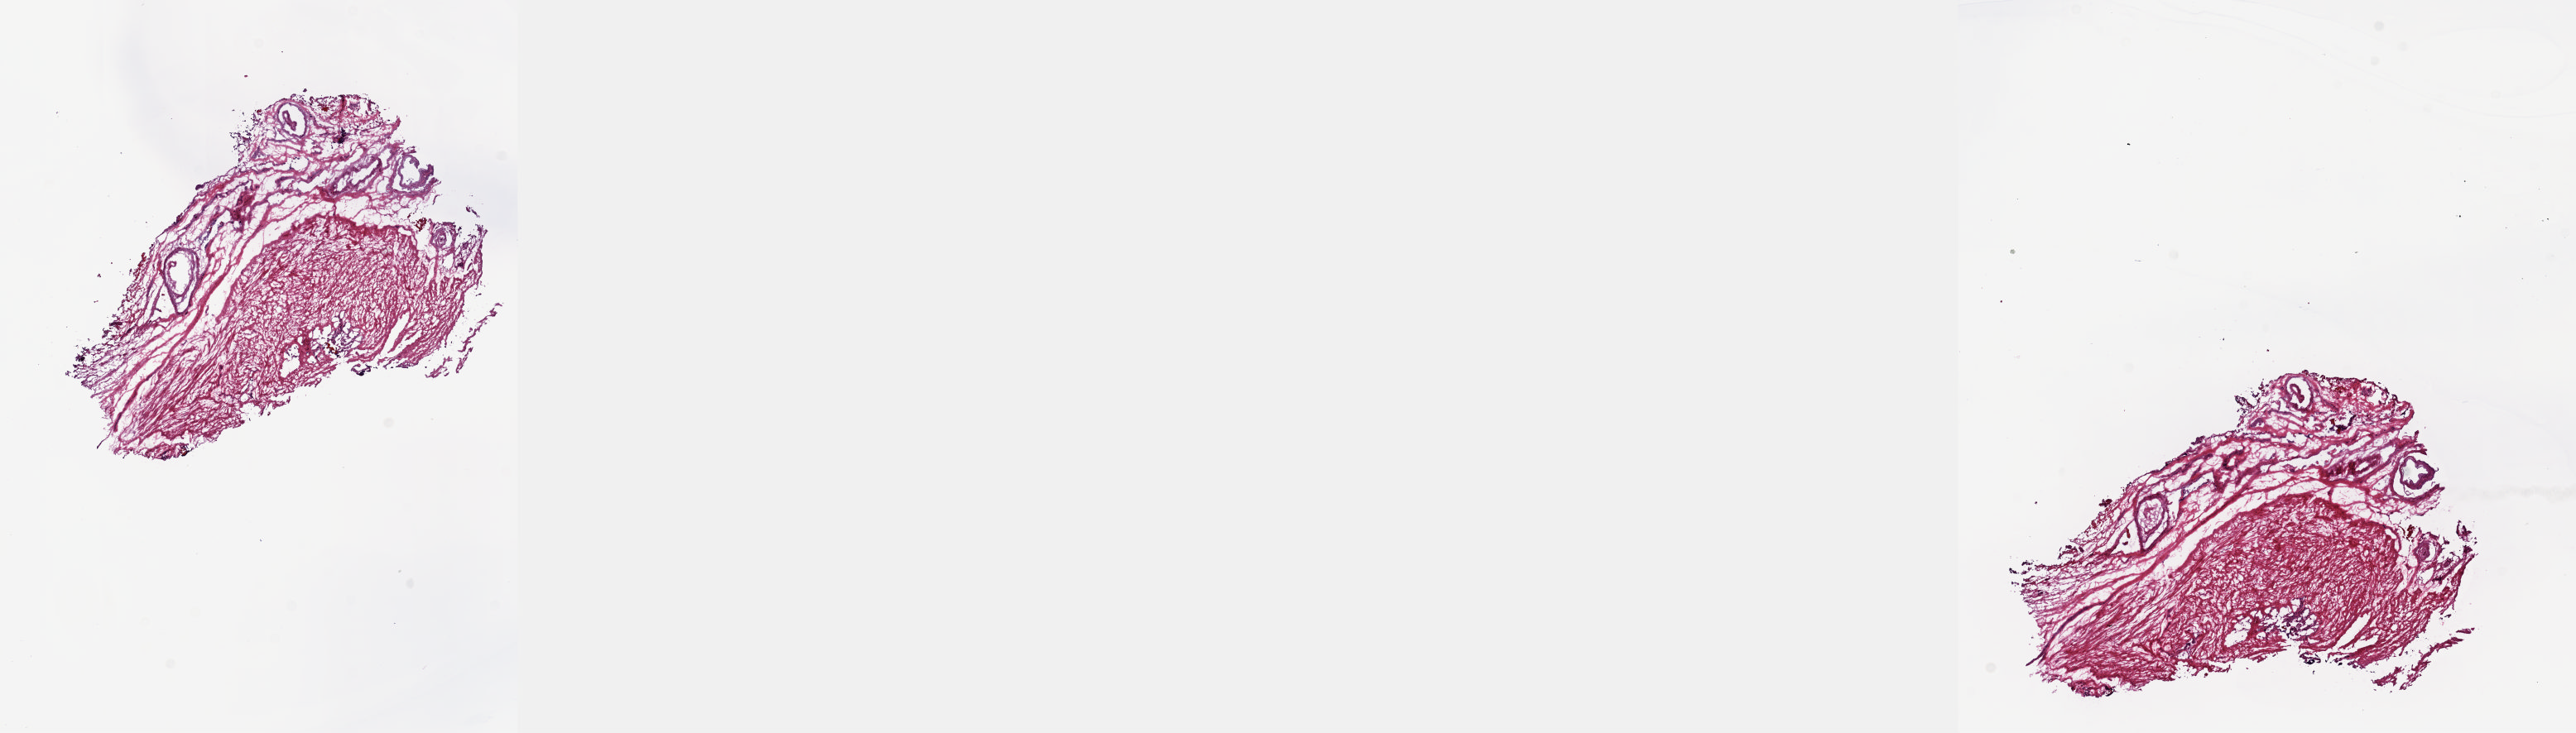
H&E-stained whole-slide image, shown as a low-resolution overview of the whole scanned area (about 25.1 x 7.1 mm), frozen section from the top of the tissue portion, solid tissue normal (non-tumour tissue) sample from the prostate. Patient: male, age at initial diagnosis 65 years. Pathologist review of this section (percent, as recorded): tumour cells 0%, tumour nuclei 0%, normal cells 100%, stromal cells 0%, necrosis 0%. Inflammatory infiltration, as recorded: lymphocyte infiltration 0%, monocyte infiltration 0%, neutrophil infiltration 0%.
This section: solid tissue normal (non-tumour) sample from the same patient. Patient diagnosis: Adenocarcinoma, NOS (prostate gland).